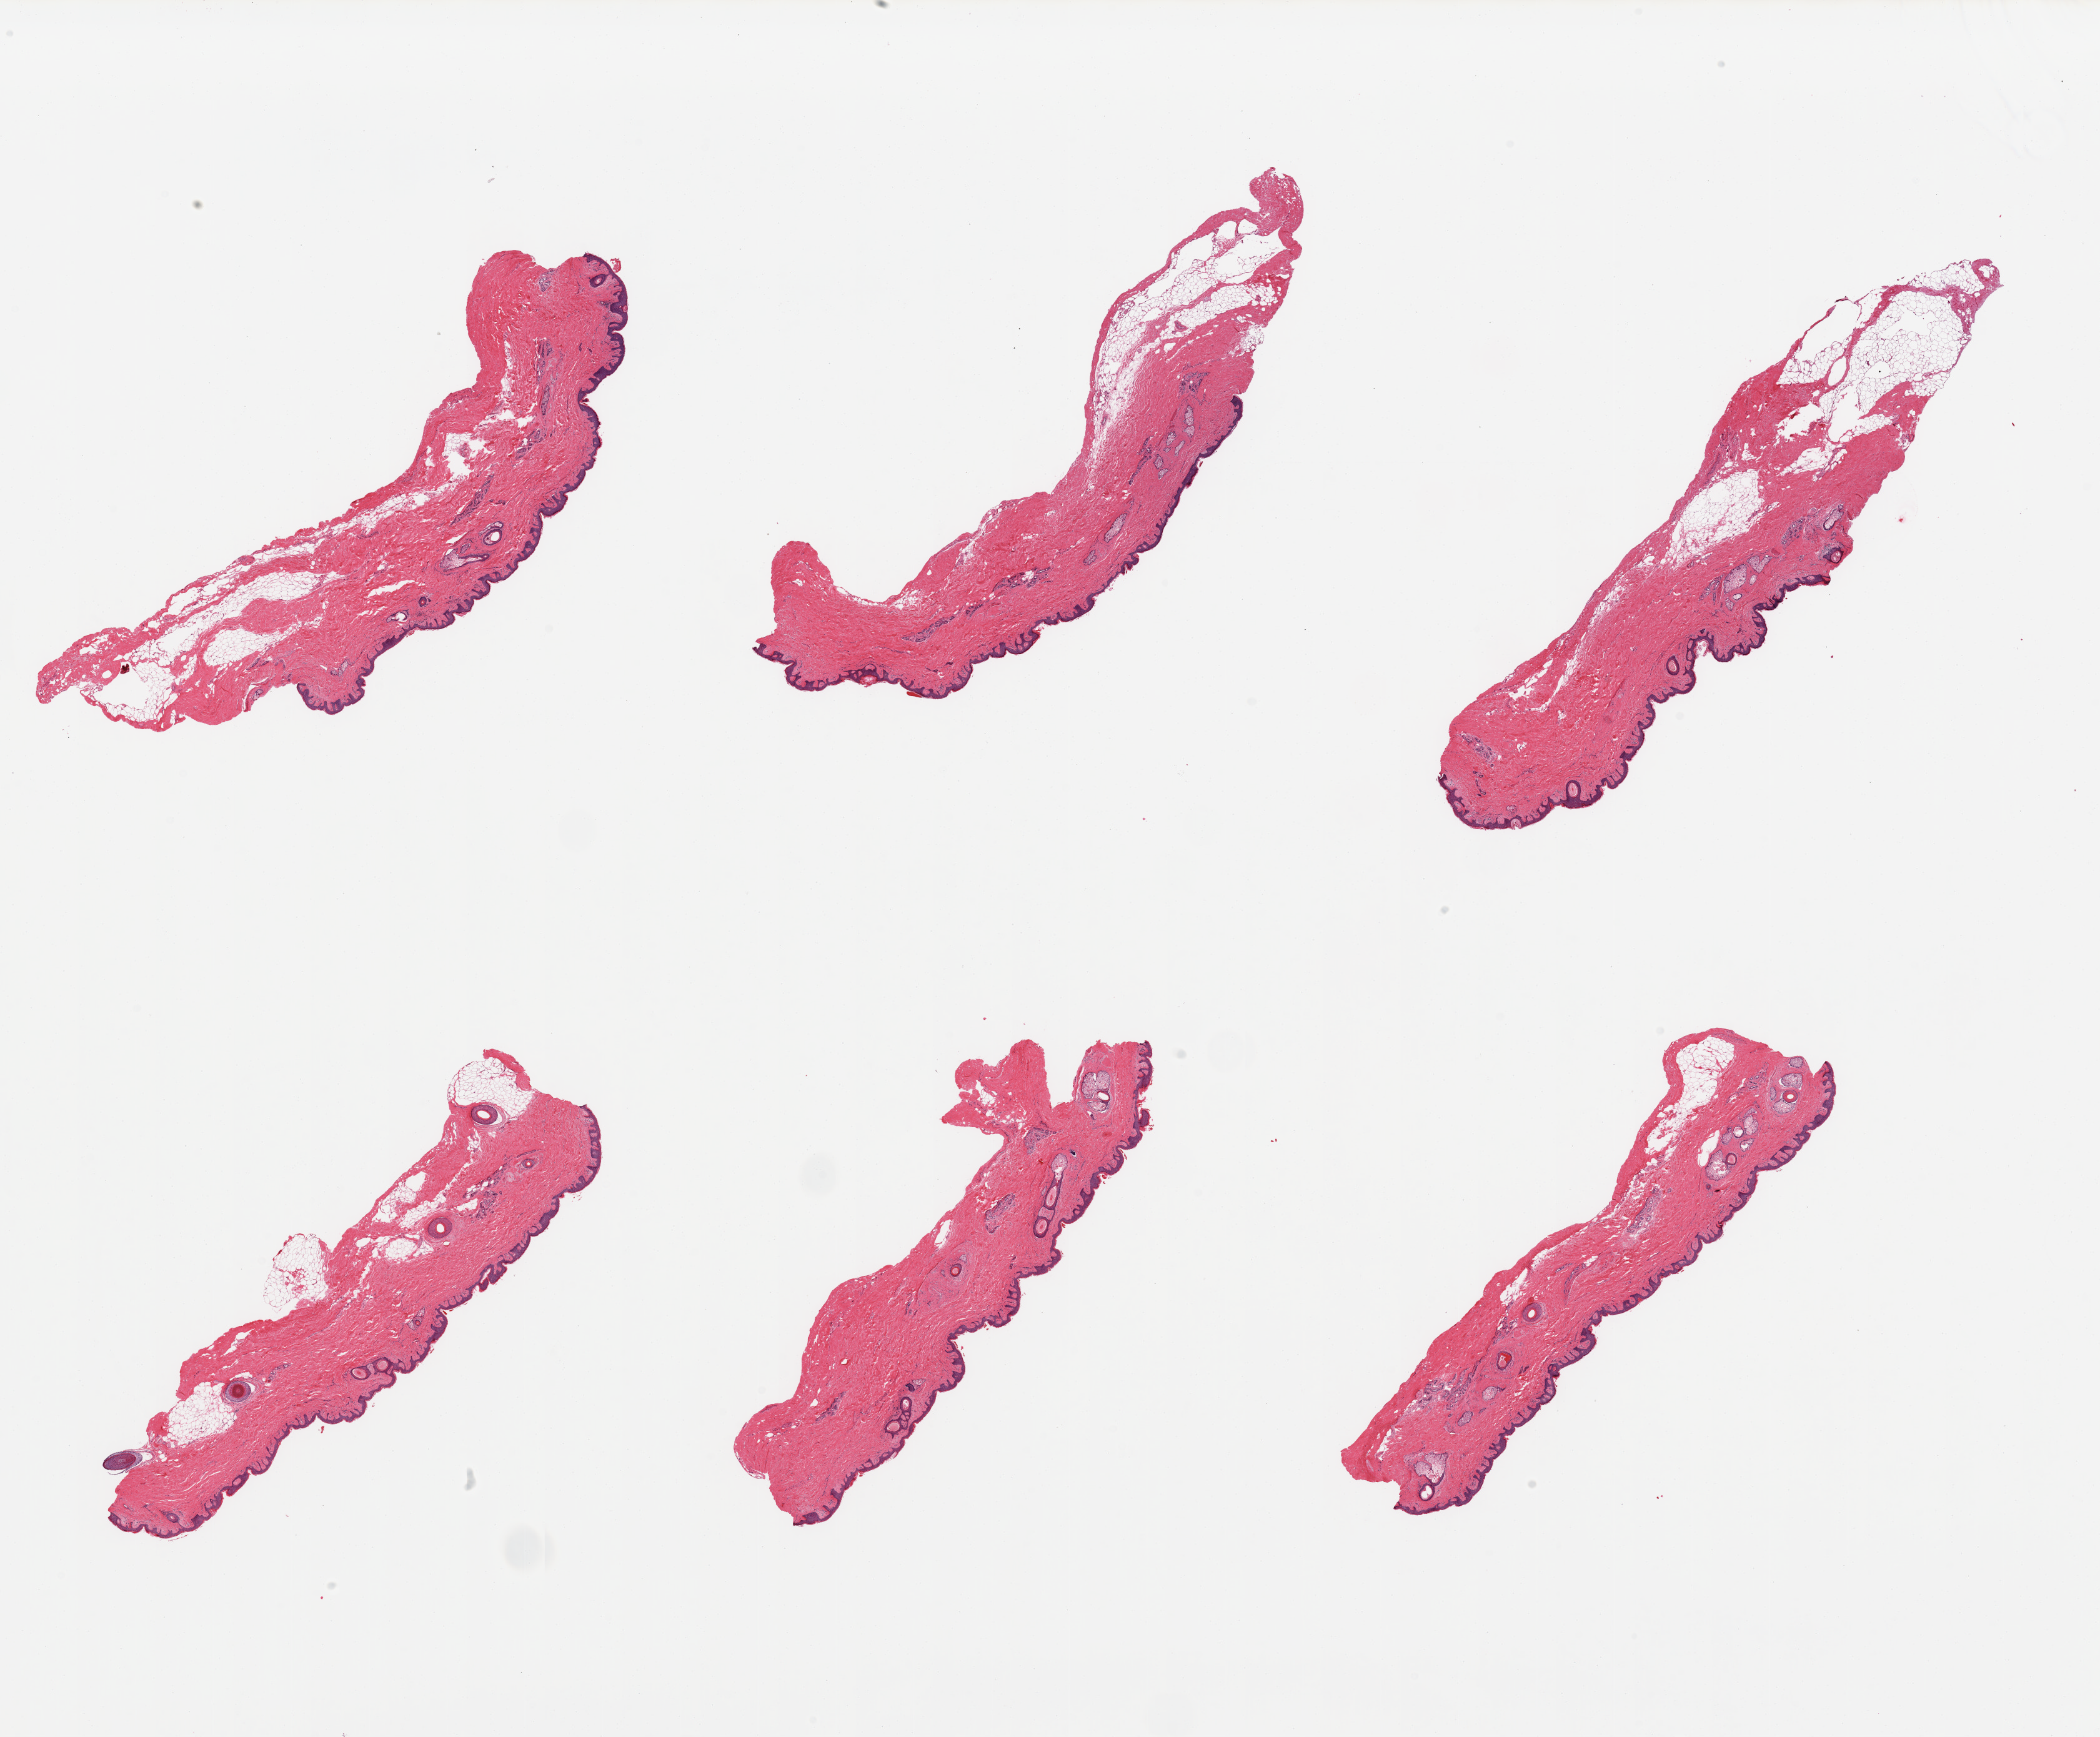
Digitized haematoxylin and eosin-stained section, a low-resolution overview of the entire scanned area, about 26.6 x 22.0 mm; PAXgene-fixed, paraffin-embedded tissue; sampled site (target tissue): skin of suprapubic region; donor tissue sample. Donor: male.
Pathologist's review note for this sample: 6 pieces; include 10-30% internal/attached fat.